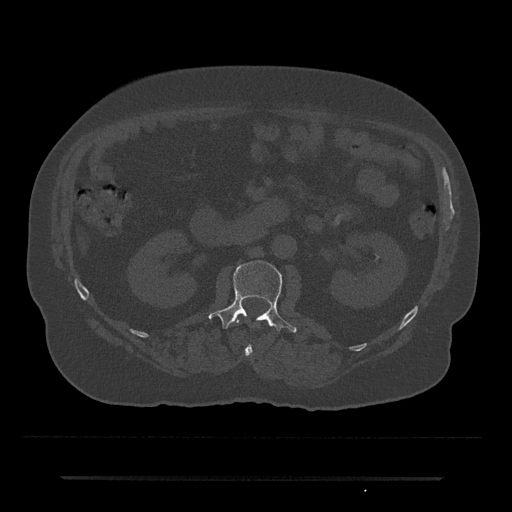
CT including the spine, one axial slice; slice 22 of 797 in the series (ordered by position); reconstruction kernel Br40s/3; 120 kVp; bone window (W 1800 / L 400 HU); 0.5 mm slice thickness; 512 × 512 image matrix, field of view 437 × 437 mm. Male patient, age 69 years. From the clinical record (not read from this slice): primary cancer: prostate.
Structures marked on this image (semi-automatic segmentation, software-assisted and operator-edited):
- L1 vertebra: bounding box <236,317,253,357> (left, top, right, bottom; pixels)
- L2 vertebra: <209,261,297,333>